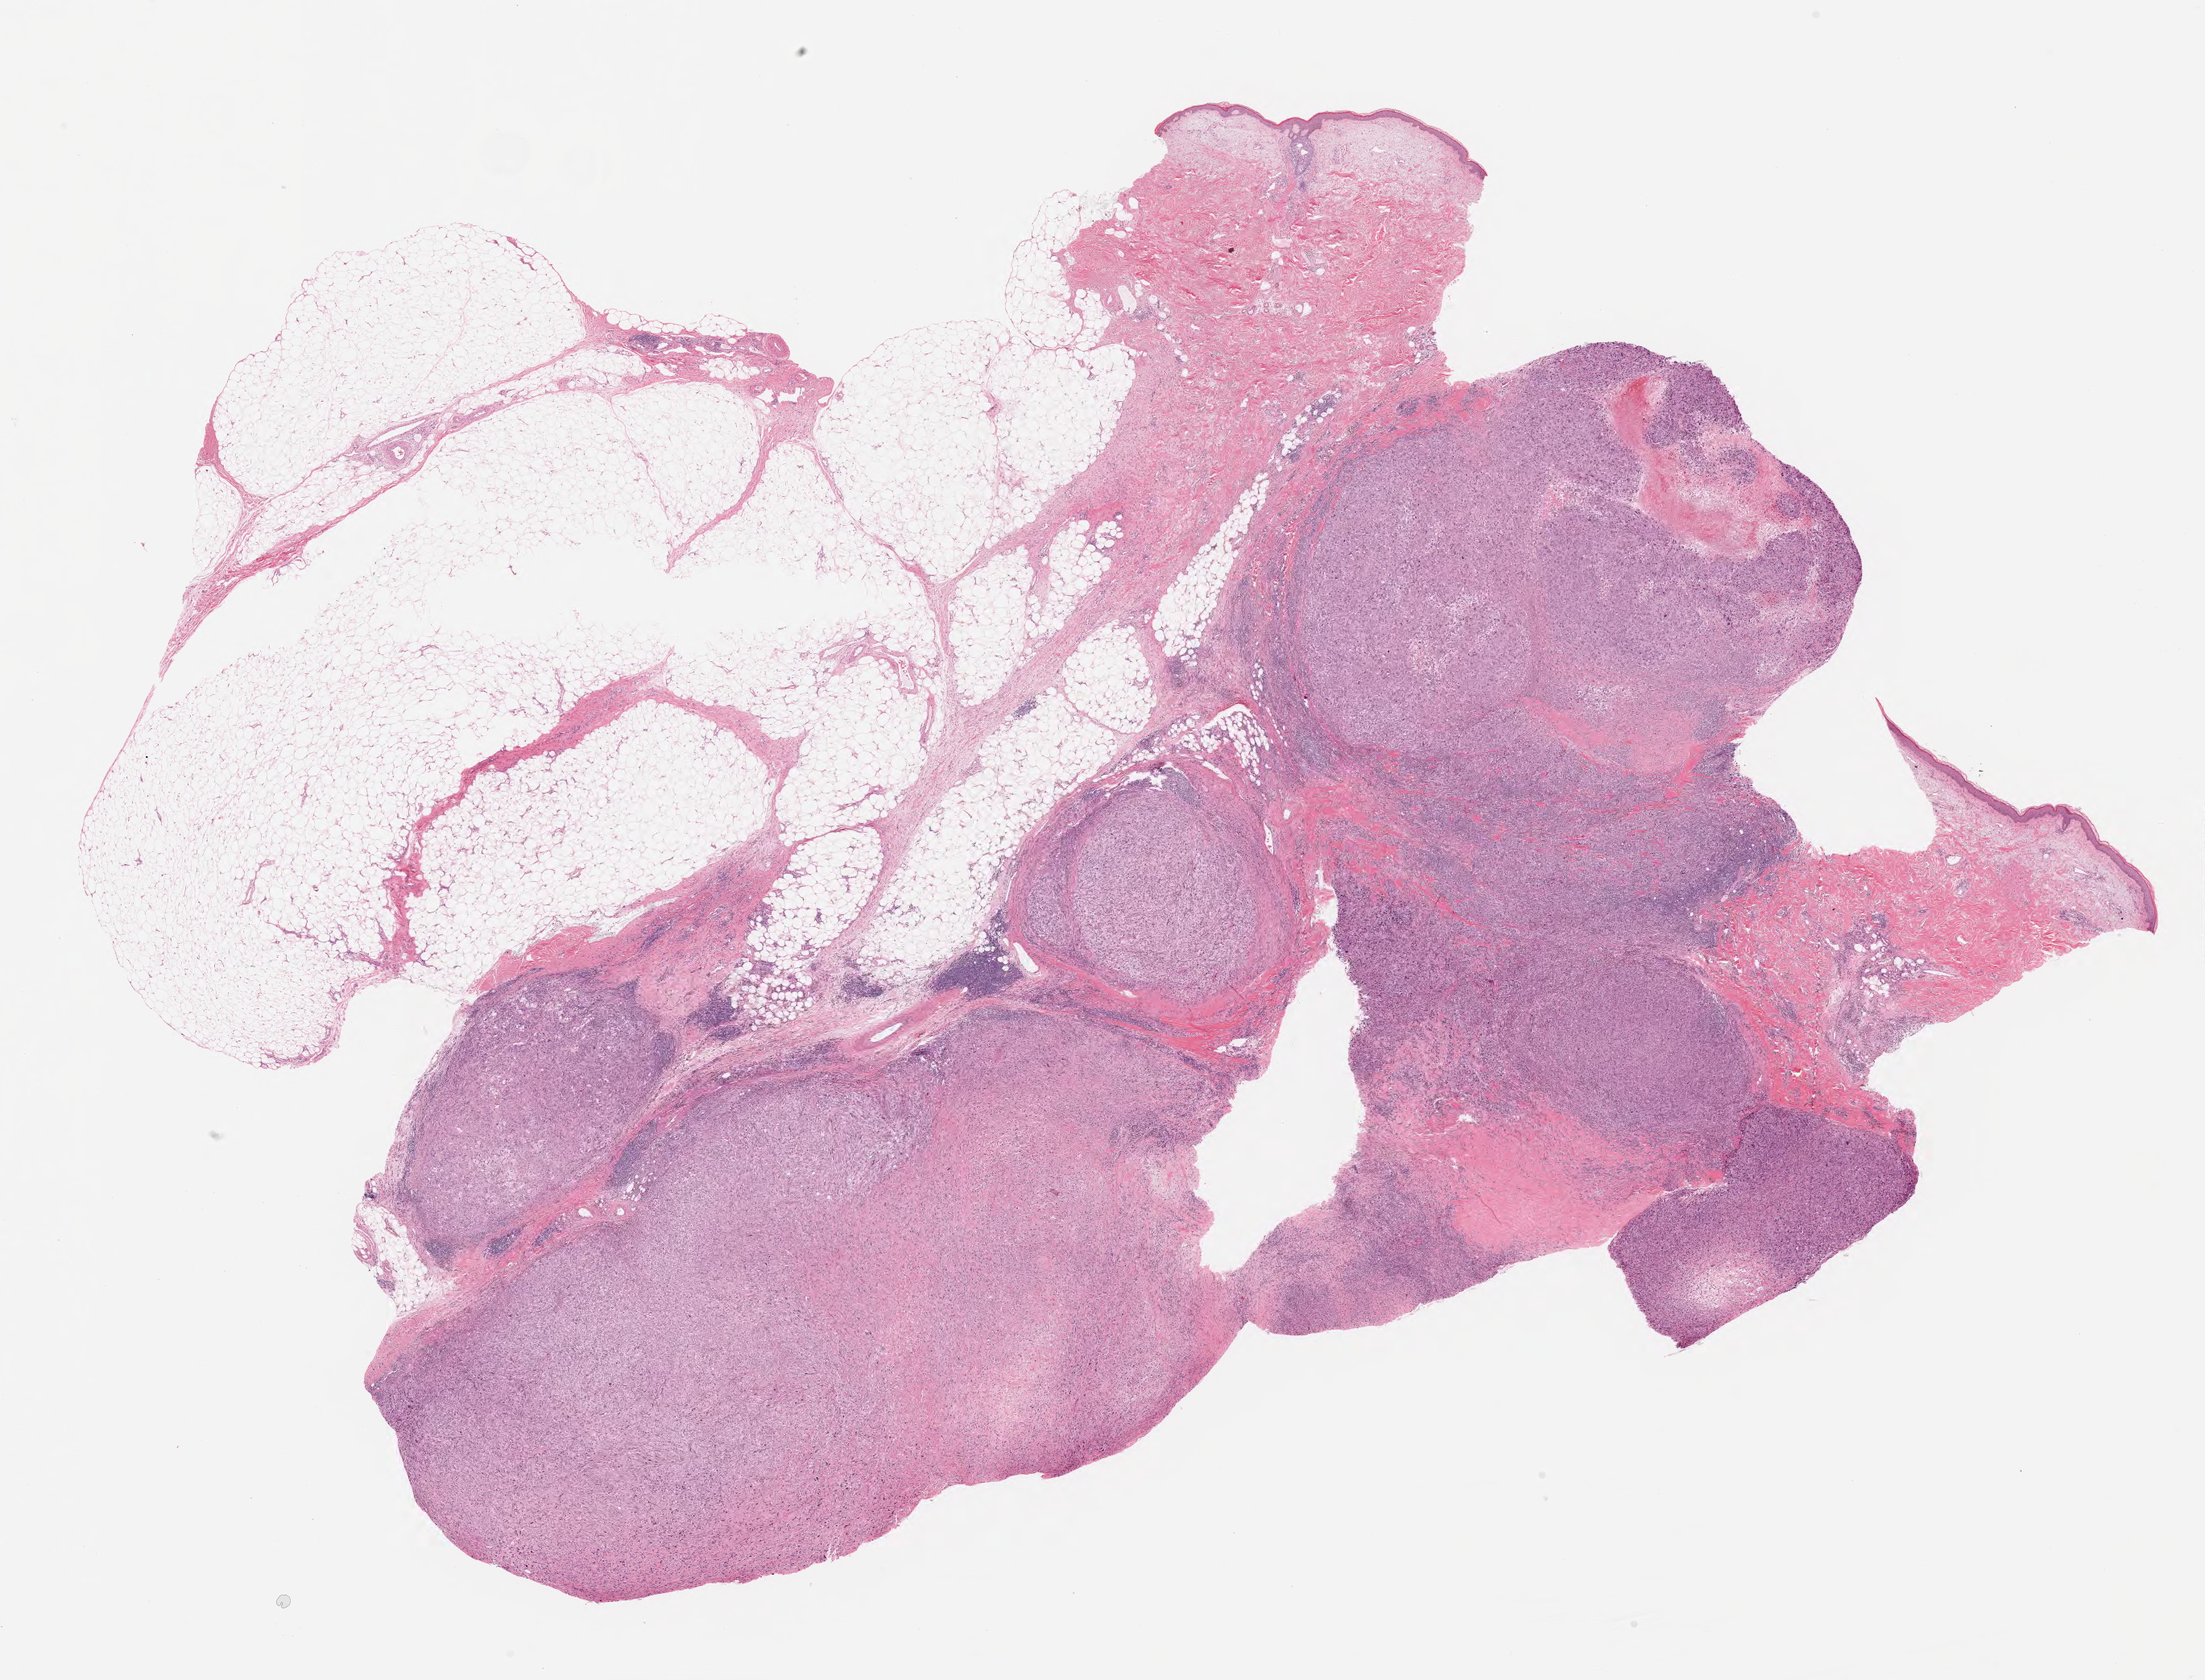
Digitized H&E tissue section (whole slide), a low-resolution overview of the entire scanned area, about 21.6 x 16.5 mm. Formalin-fixed paraffin-embedded (FFPE) diagnostic section. Sample: primary tumour, connective, subcutaneous and other soft tissues. Male, age 78 years at initial diagnosis.
Diagnosis: Undifferentiated sarcoma (connective, subcutaneous and other soft tissues of upper limb and shoulder).